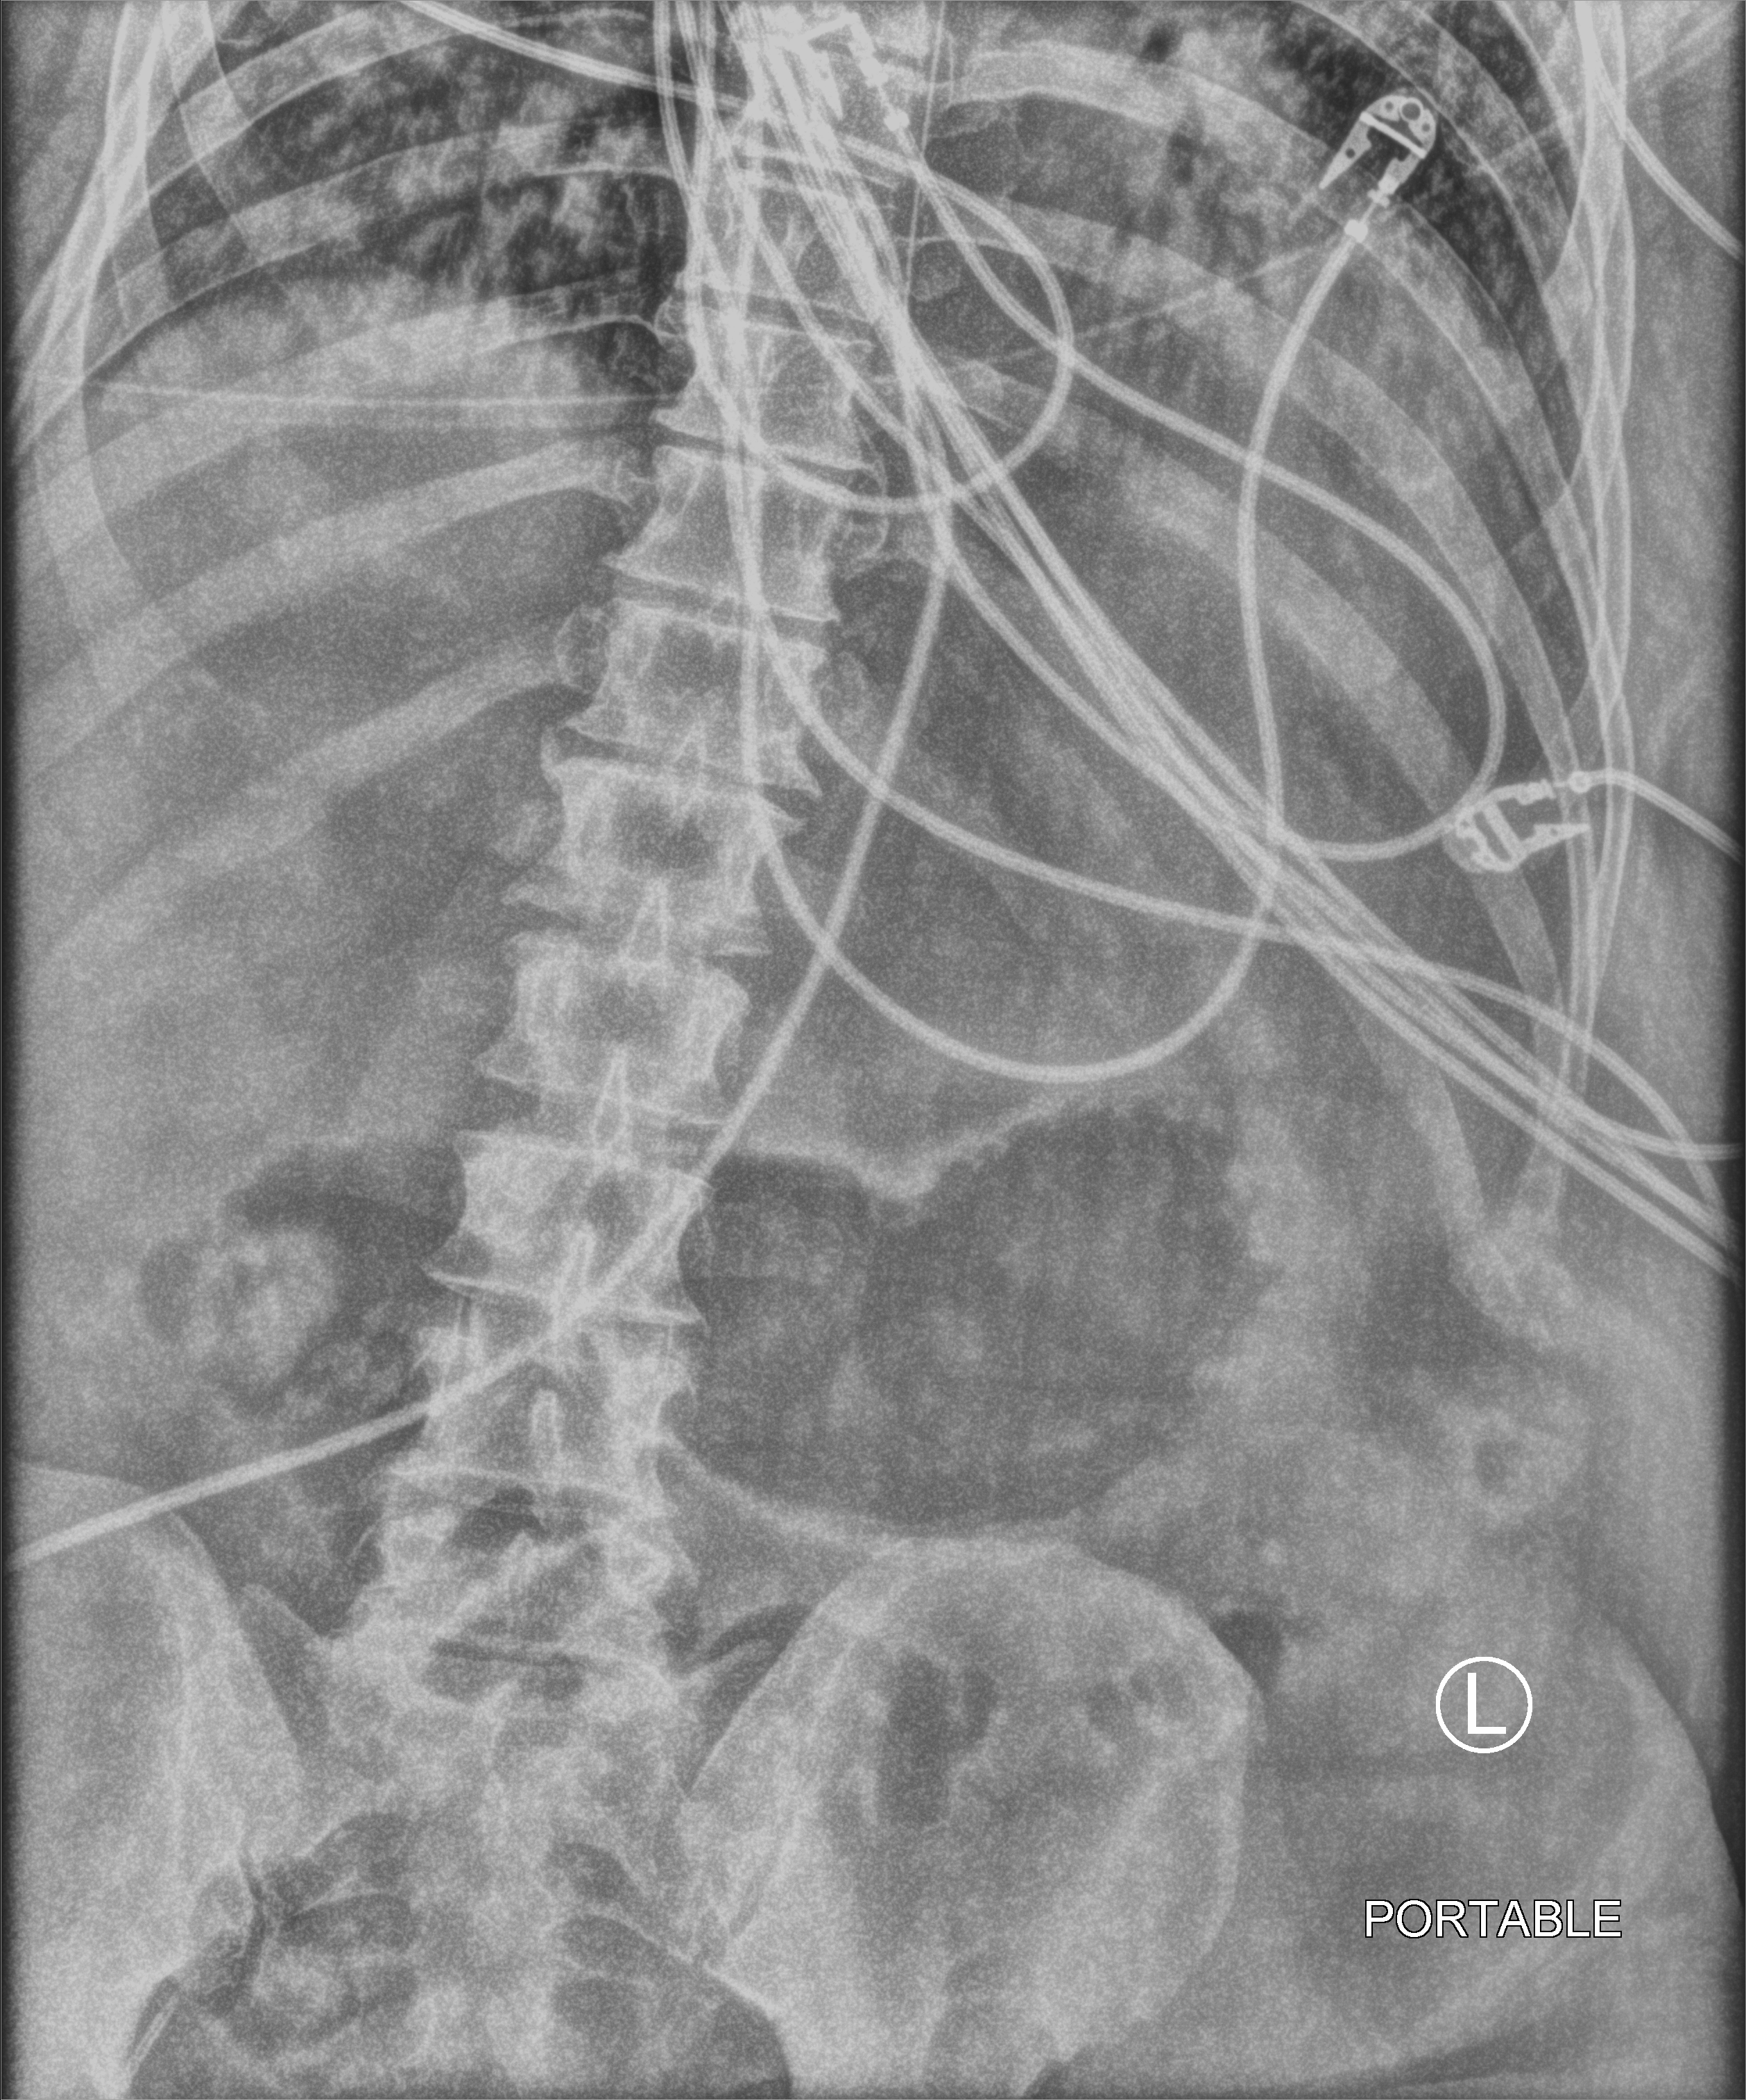
Abdomen X-ray (portable); anteroposterior (AP) projection. Male patient hospitalised with COVID-19, age 60–74 years.
From the hospital-stay record, not from the radiograph (when in the stay this image was taken is not recorded): chronic kidney disease (admission record): no; mechanically ventilated during this hospital stay: yes.